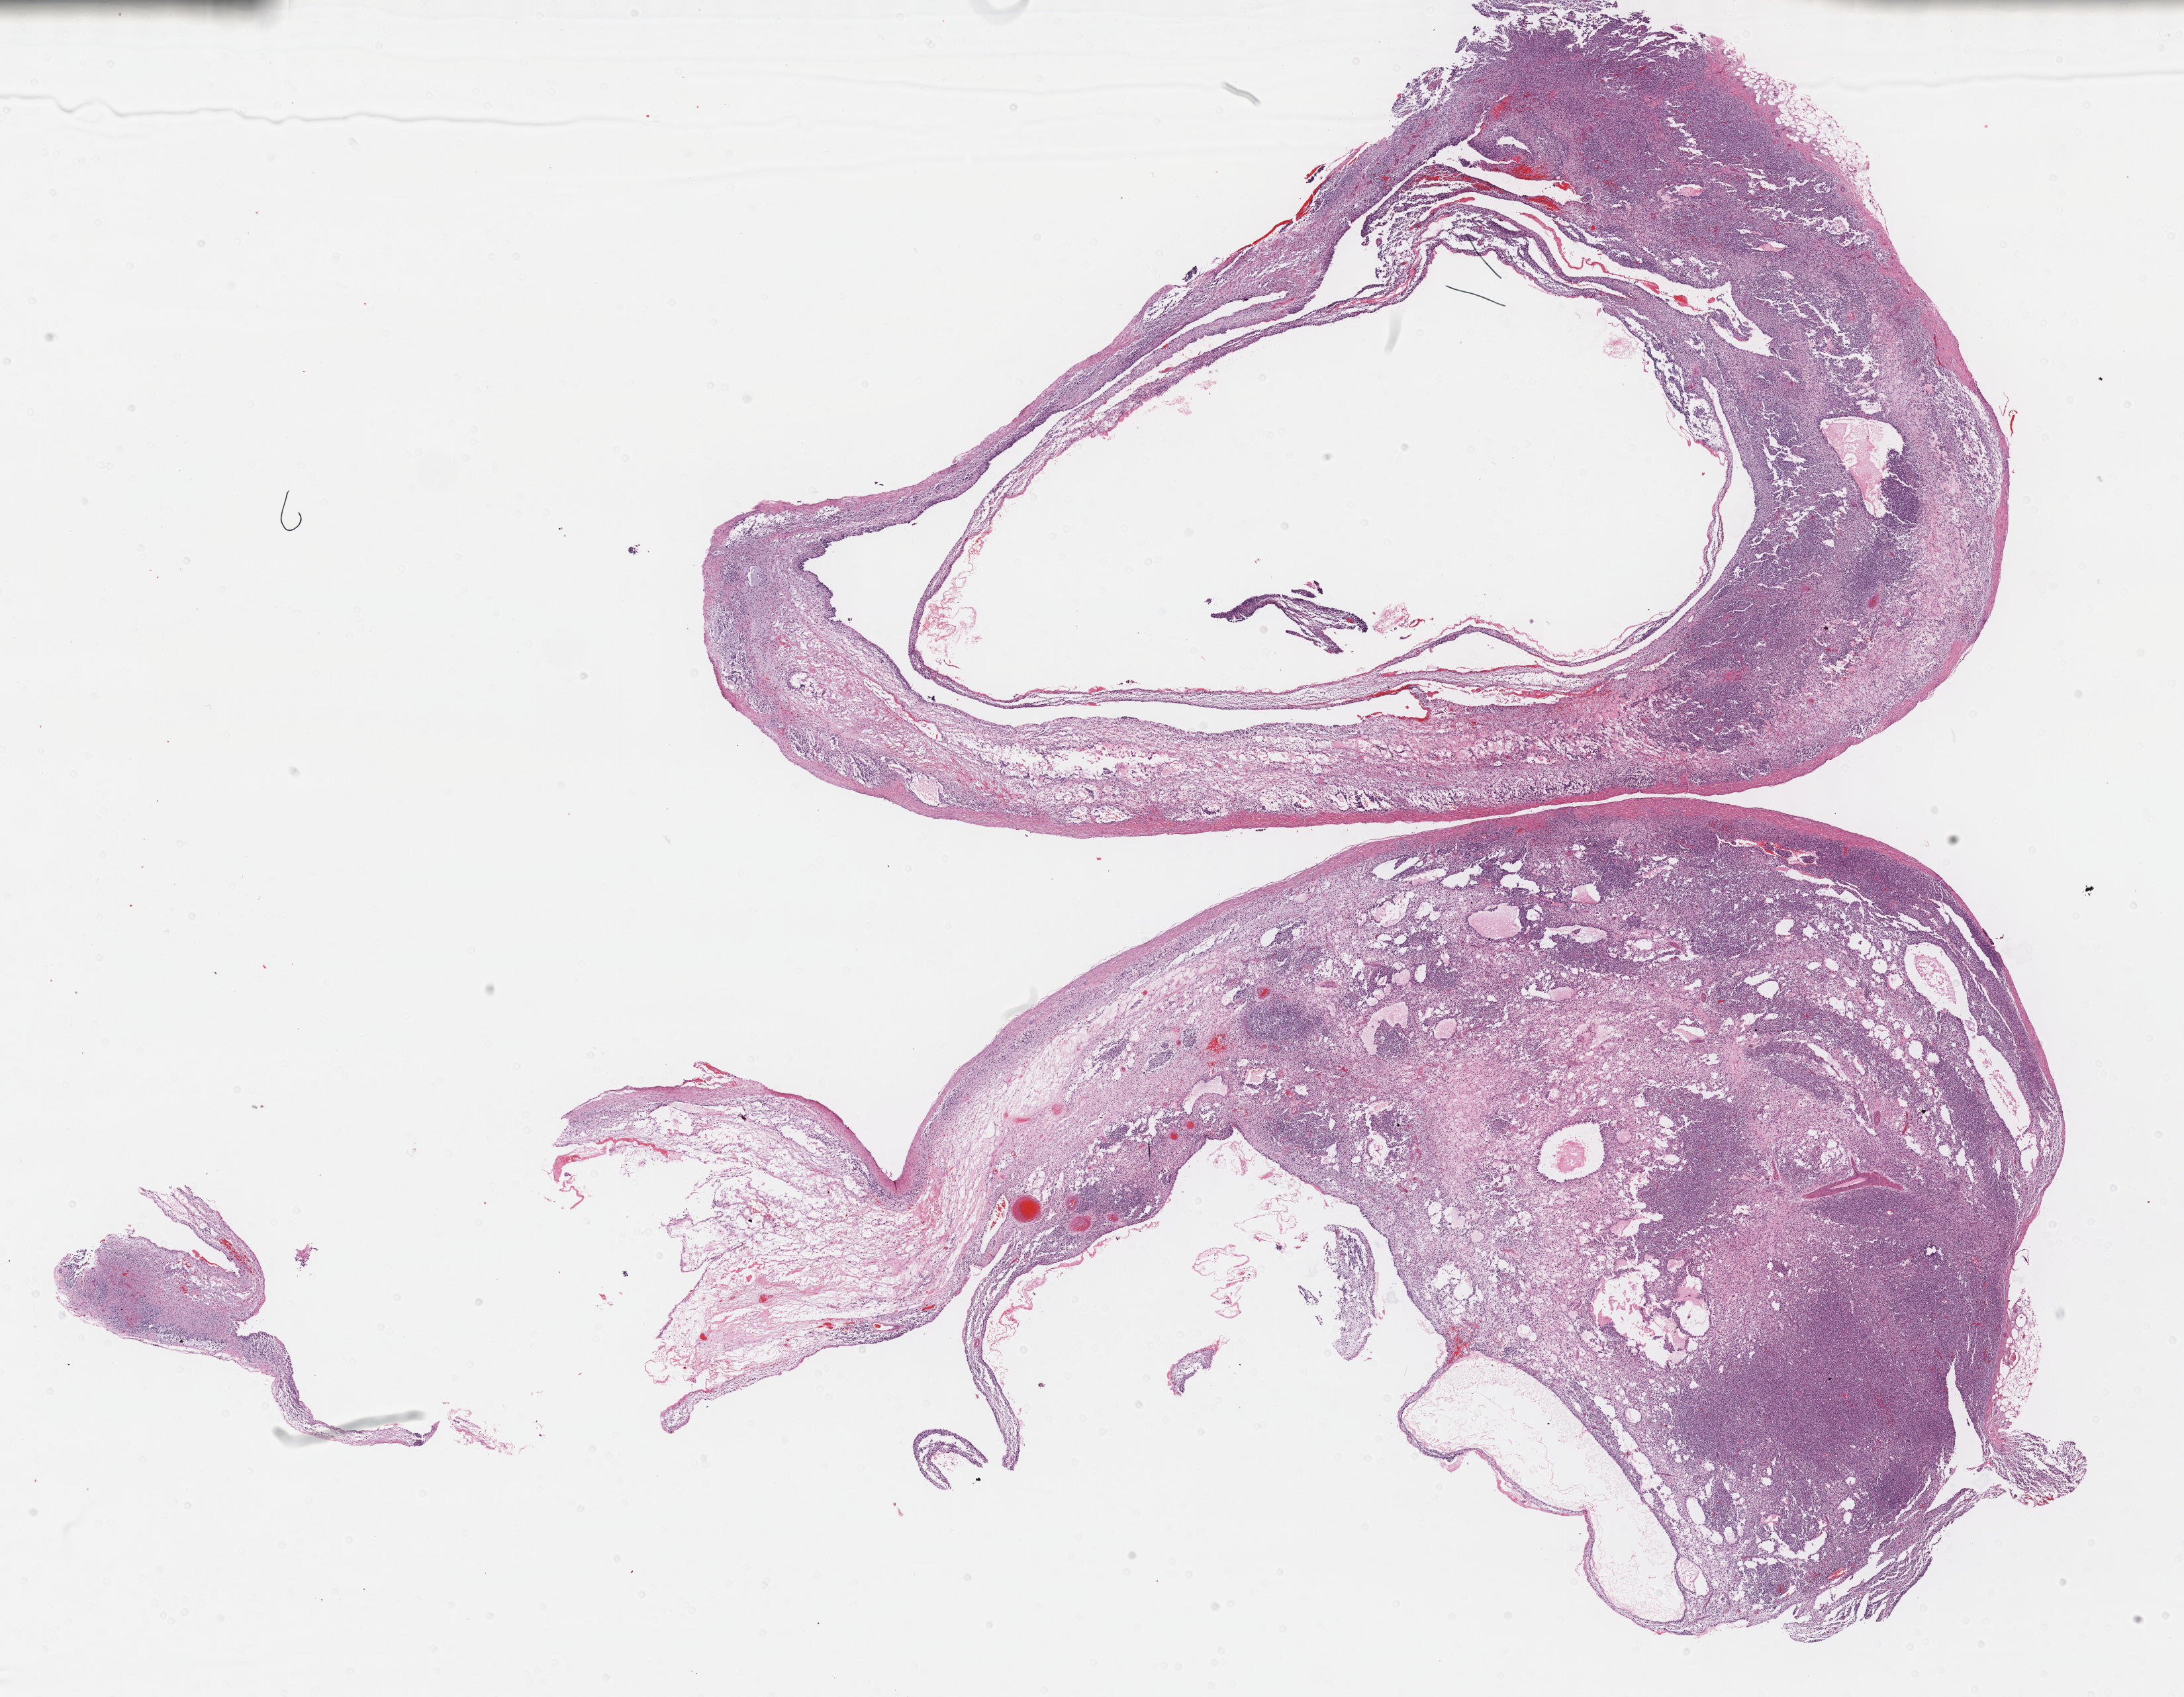
Whole-slide histology image, Hematoxylin and eosin (H&E) stained — shown as a low-resolution overview of the whole scanned area (about 26.7 x 20.7 mm, acquisition: 40x scan). FFPE section. Retroperitoneum and peritoneum, primary tumour sample. Male, age 57 years at initial diagnosis.
* pathologic diagnosis: Dedifferentiated liposarcoma (retroperitoneum)